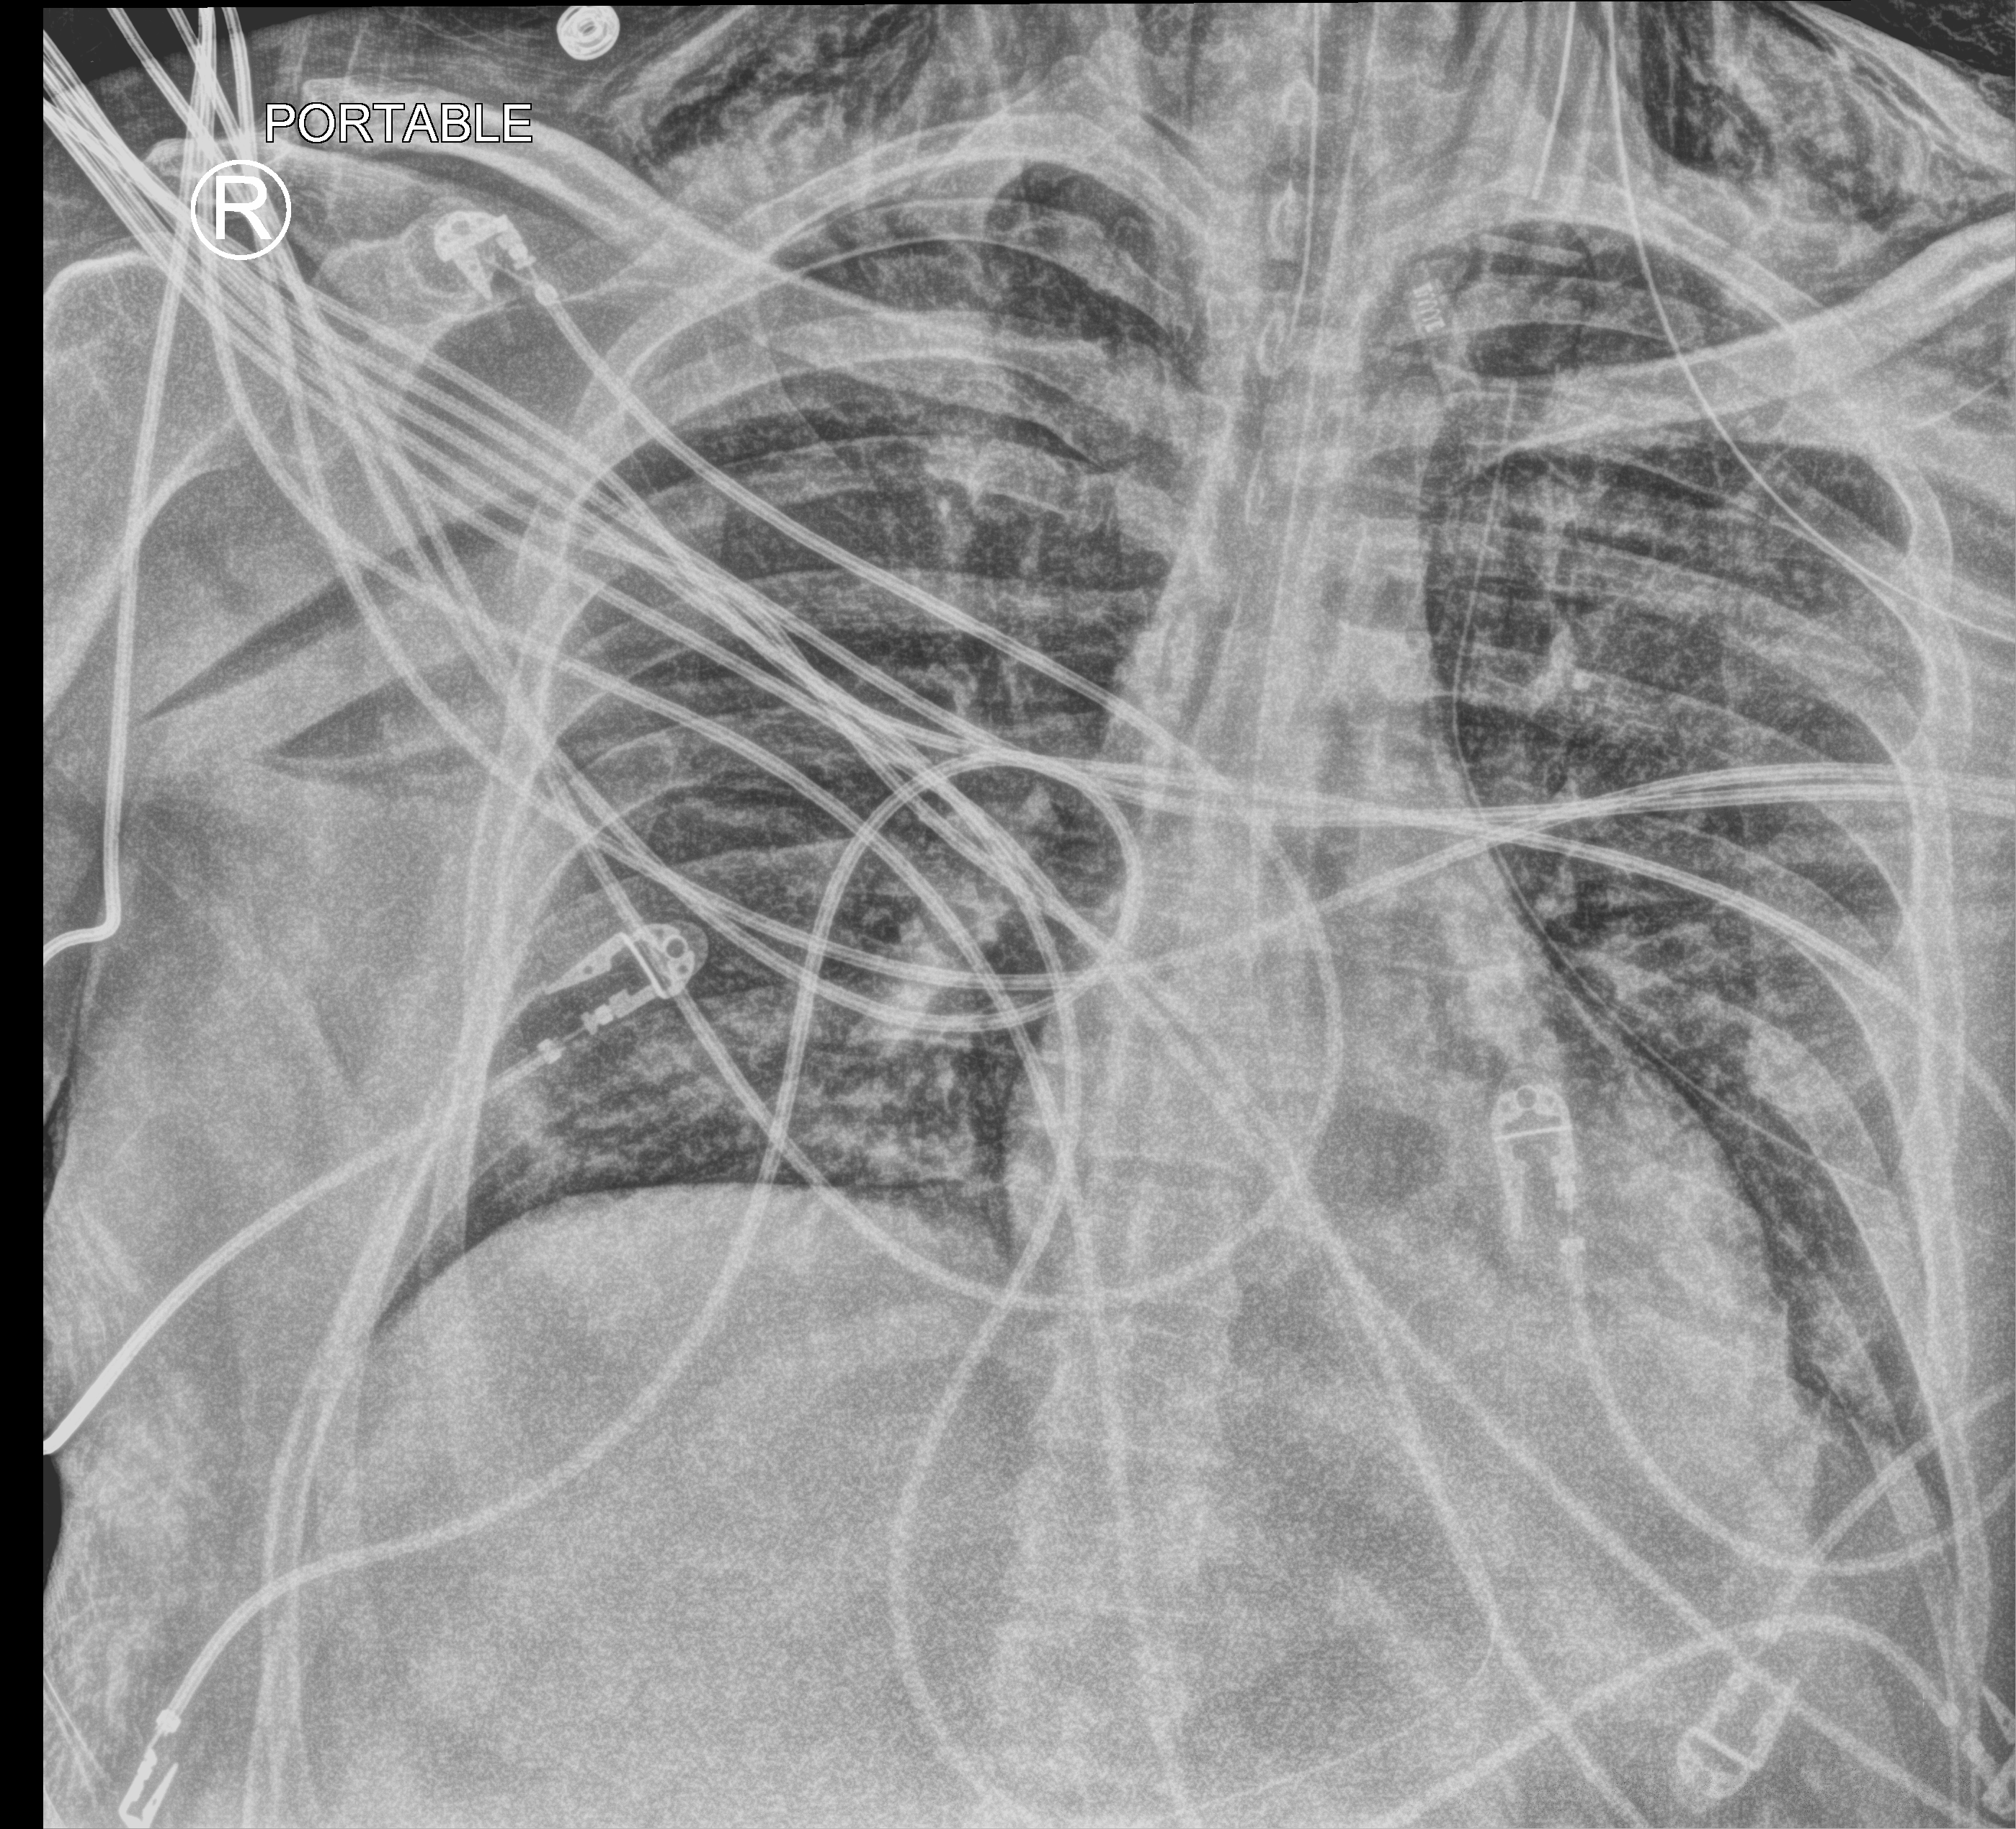
Chest X-ray (portable), anteroposterior (AP) projection. Male patient hospitalised with COVID-19, age 18–59 years.
Hospital-stay facts (about this admission, not read from this image; timing relative to this image not recorded):
- mechanically ventilated during this hospital stay: yes